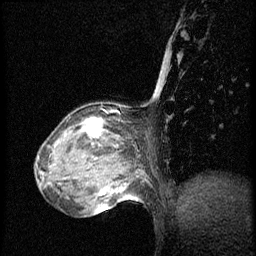
Breast MRI (dynamic contrast-enhanced), one sagittal slice. Position 19 of 56 along the scan axis. Dynamic contrast-enhanced series, image 2 of 3 at this slice position (ordered by acquisition). 1.5 T. TE 4.2 ms, TR 20.4 ms. 2 mm slice thickness. 256 × 256 image matrix. Patient: female, 64 years. From the clinical record (not read from this slice): setting: breast cancer imaged before/during neoadjuvant chemotherapy; receptor status: HR-positive, HER2-negative.
Annotated regions visible in this slice (semi-automatically segmented with operator editing):
- analysis volume of interest (the breast-tissue region the enhancement analysis was run in; not a lesion): bounding box [x1, y1, x2, y2] px = [48, 103, 142, 186]
- tumour enhancement mask (voxels above the 70 % enhancement threshold inside the analysis volume of interest): [83, 117, 103, 137]